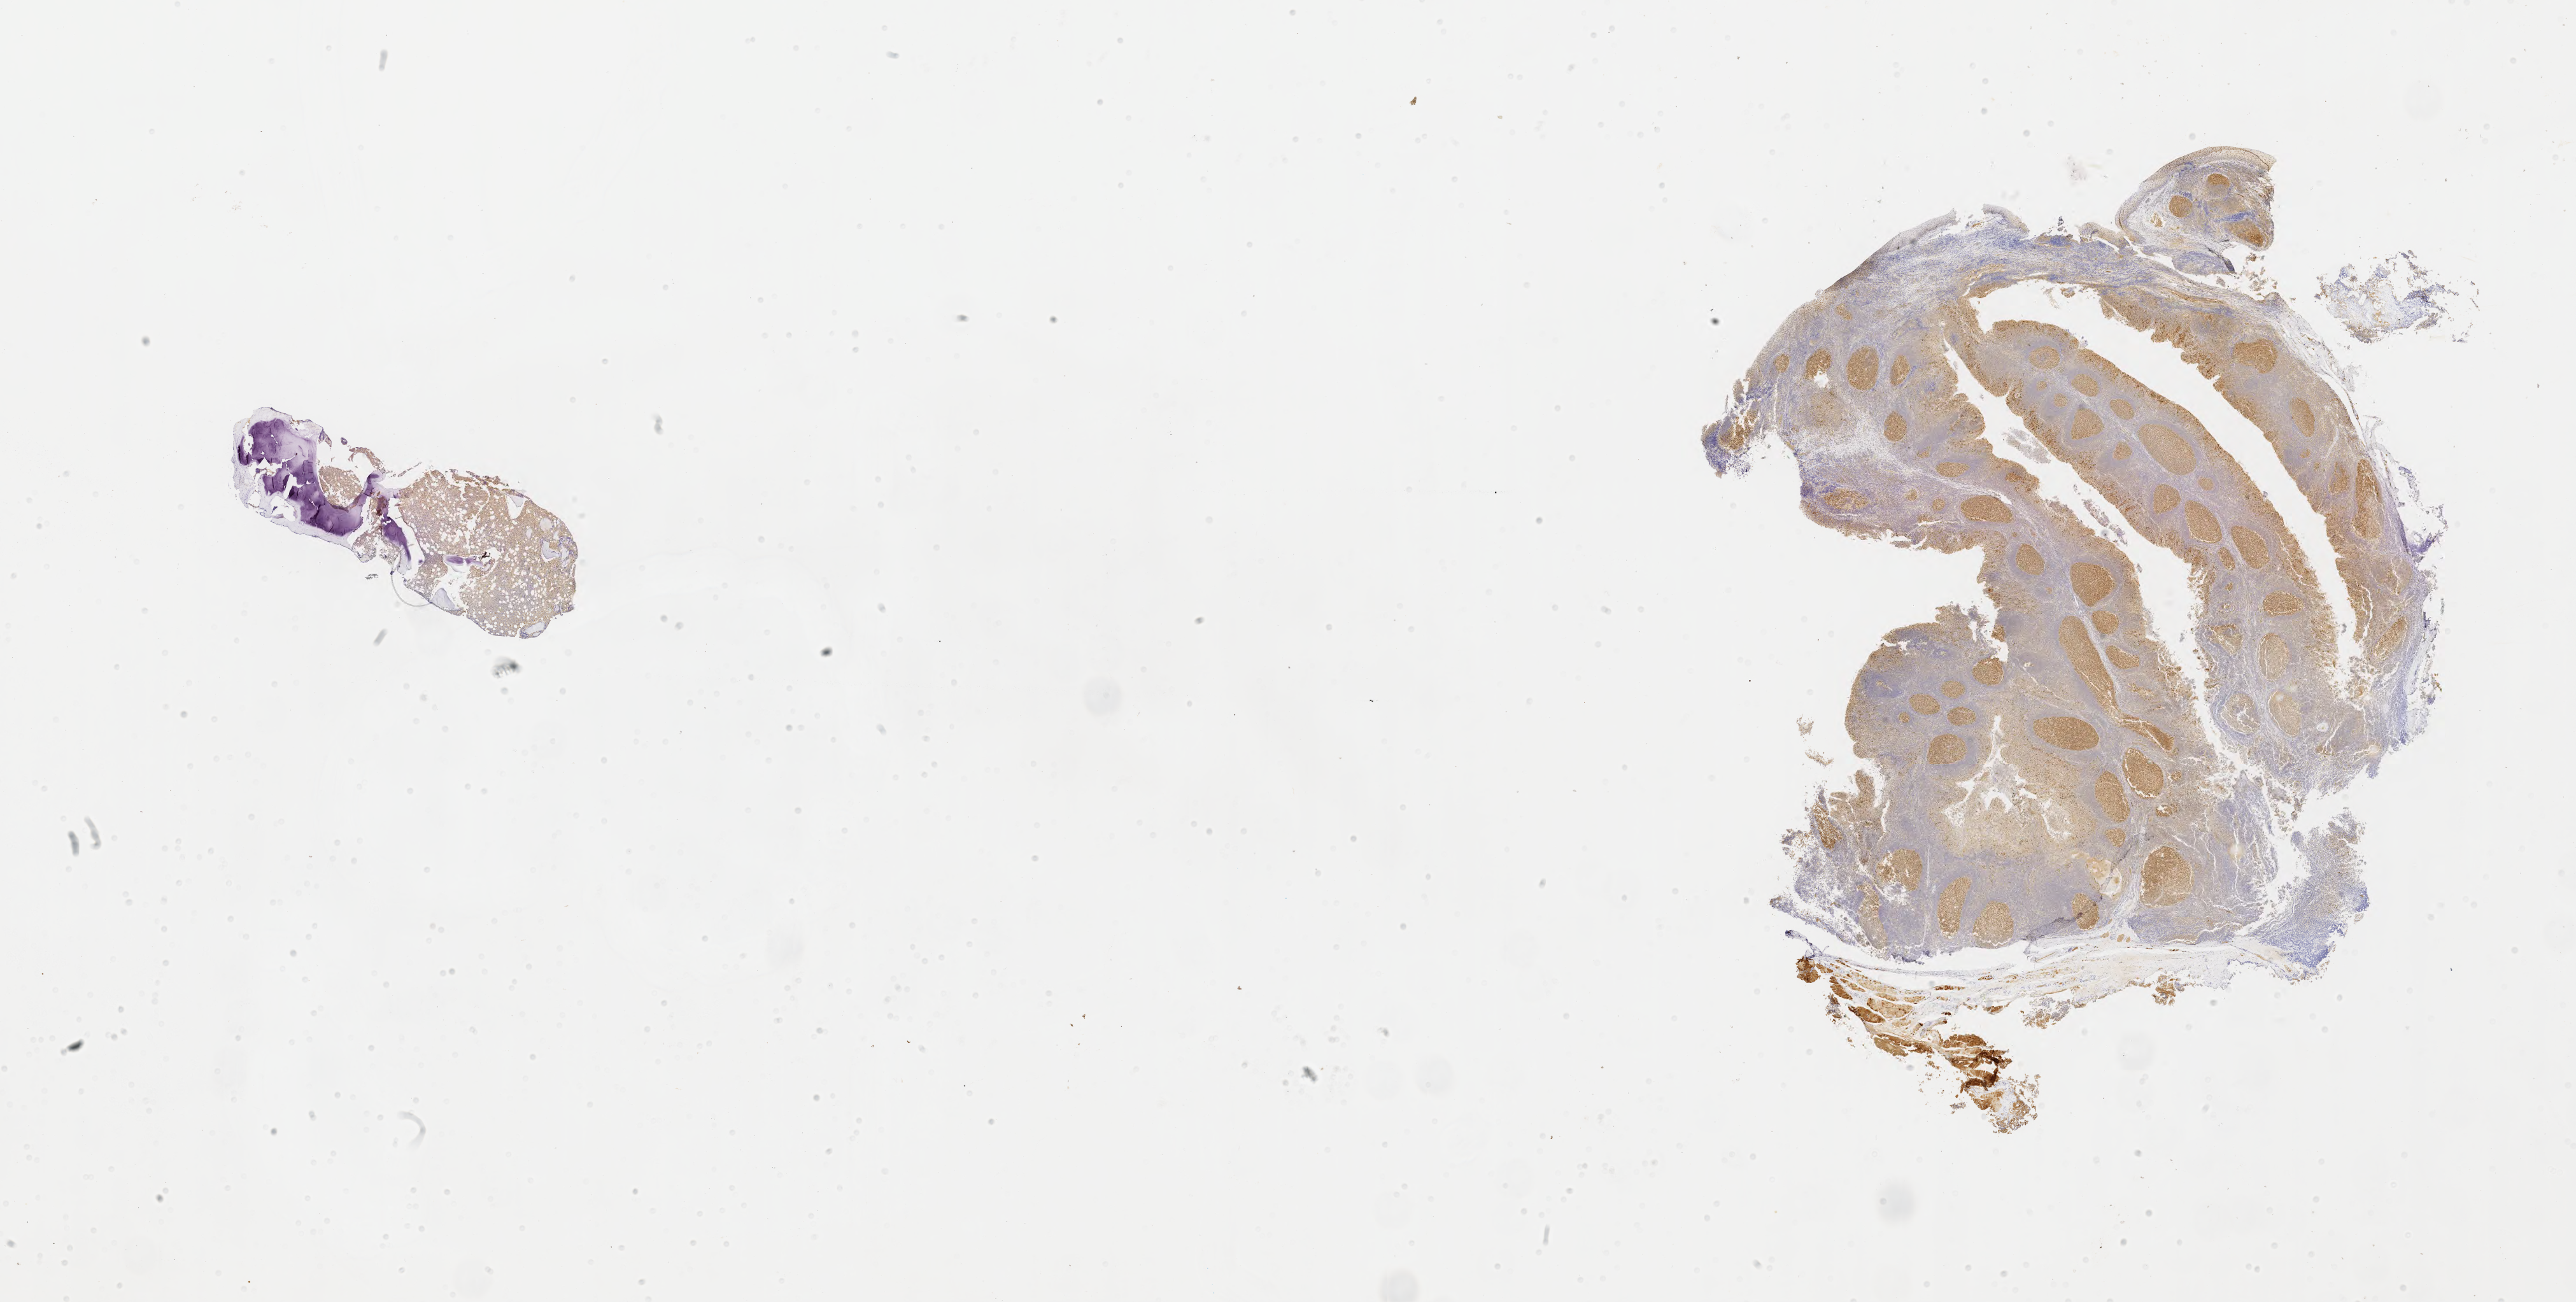
Whole-slide image, immunohistochemical stain for BCL6 — shown as a low-resolution overview of the whole scanned area (about 32.7 x 16.5 mm). Specimen: tumor tissue. Site: bone marrow. Patient male; 15 years old.
Diagnosis: Burkitt lymphoma, NOS.